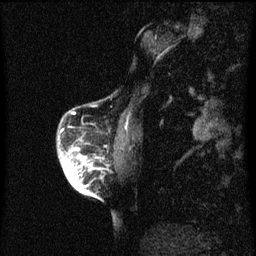
Breast MRI (dynamic contrast-enhanced), one sagittal slice; slice 15 of 60 in the series (ordered by position); dynamic contrast-enhanced series, image 2 of 3 at this slice position (ordered by acquisition); 1.5 T; TE 4.2 ms, TR 8 ms; 256 × 256 image matrix, field of view 180 × 180 mm. Female patient, age 56 years.
Structures marked on this image (semi-automatic segmentation, software-assisted and operator-edited):
- analysis volume of interest (the breast-tissue region the enhancement analysis was run in; not a lesion): bounding box (x1, y1, x2, y2) in pixels: (57, 122, 108, 199)
- tumour enhancement mask (voxels above the 70 % enhancement threshold inside the analysis volume of interest): (66, 148, 97, 197)